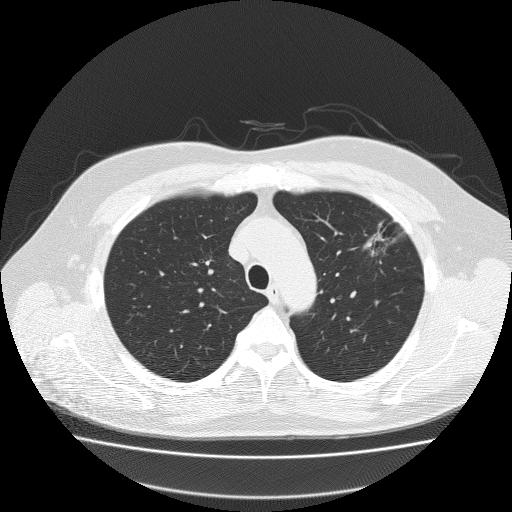
Axial slice from a low-dose chest CT screening exam, first (baseline) screen, lung window (W 1500 / L -600 HU), 2 mm slice thickness, lung (sharp) reconstruction kernel (FC51), slice 50 of 204 in the series. Male, age 62 years at enrolment. Former smoker at enrolment.
Expert-annotated lung lesion, bounding box [x1, y1, x2, y2] px = [350, 211, 418, 265]. Screening reader's record for this exam (one nodule recorded; not confirmed to be the boxed lesion): non-calcified nodule or mass ≥4 mm, left upper lobe, 18 × 8 mm, spiculated (stellate) margins, soft tissue attenuation. Official screen result: positive, change unspecified: nodule(s) >= 4 mm or enlarging nodule(s), mass(es), or other non-specific abnormalities suspicious for lung cancer. Lung cancer was diagnosed 49 days after this screen: bronchiolo-alveolar adenocarcinoma, NOS, left upper lobe, well differentiated (G1), stage IA (AJCC 6th edition), 25 mm at pathology.